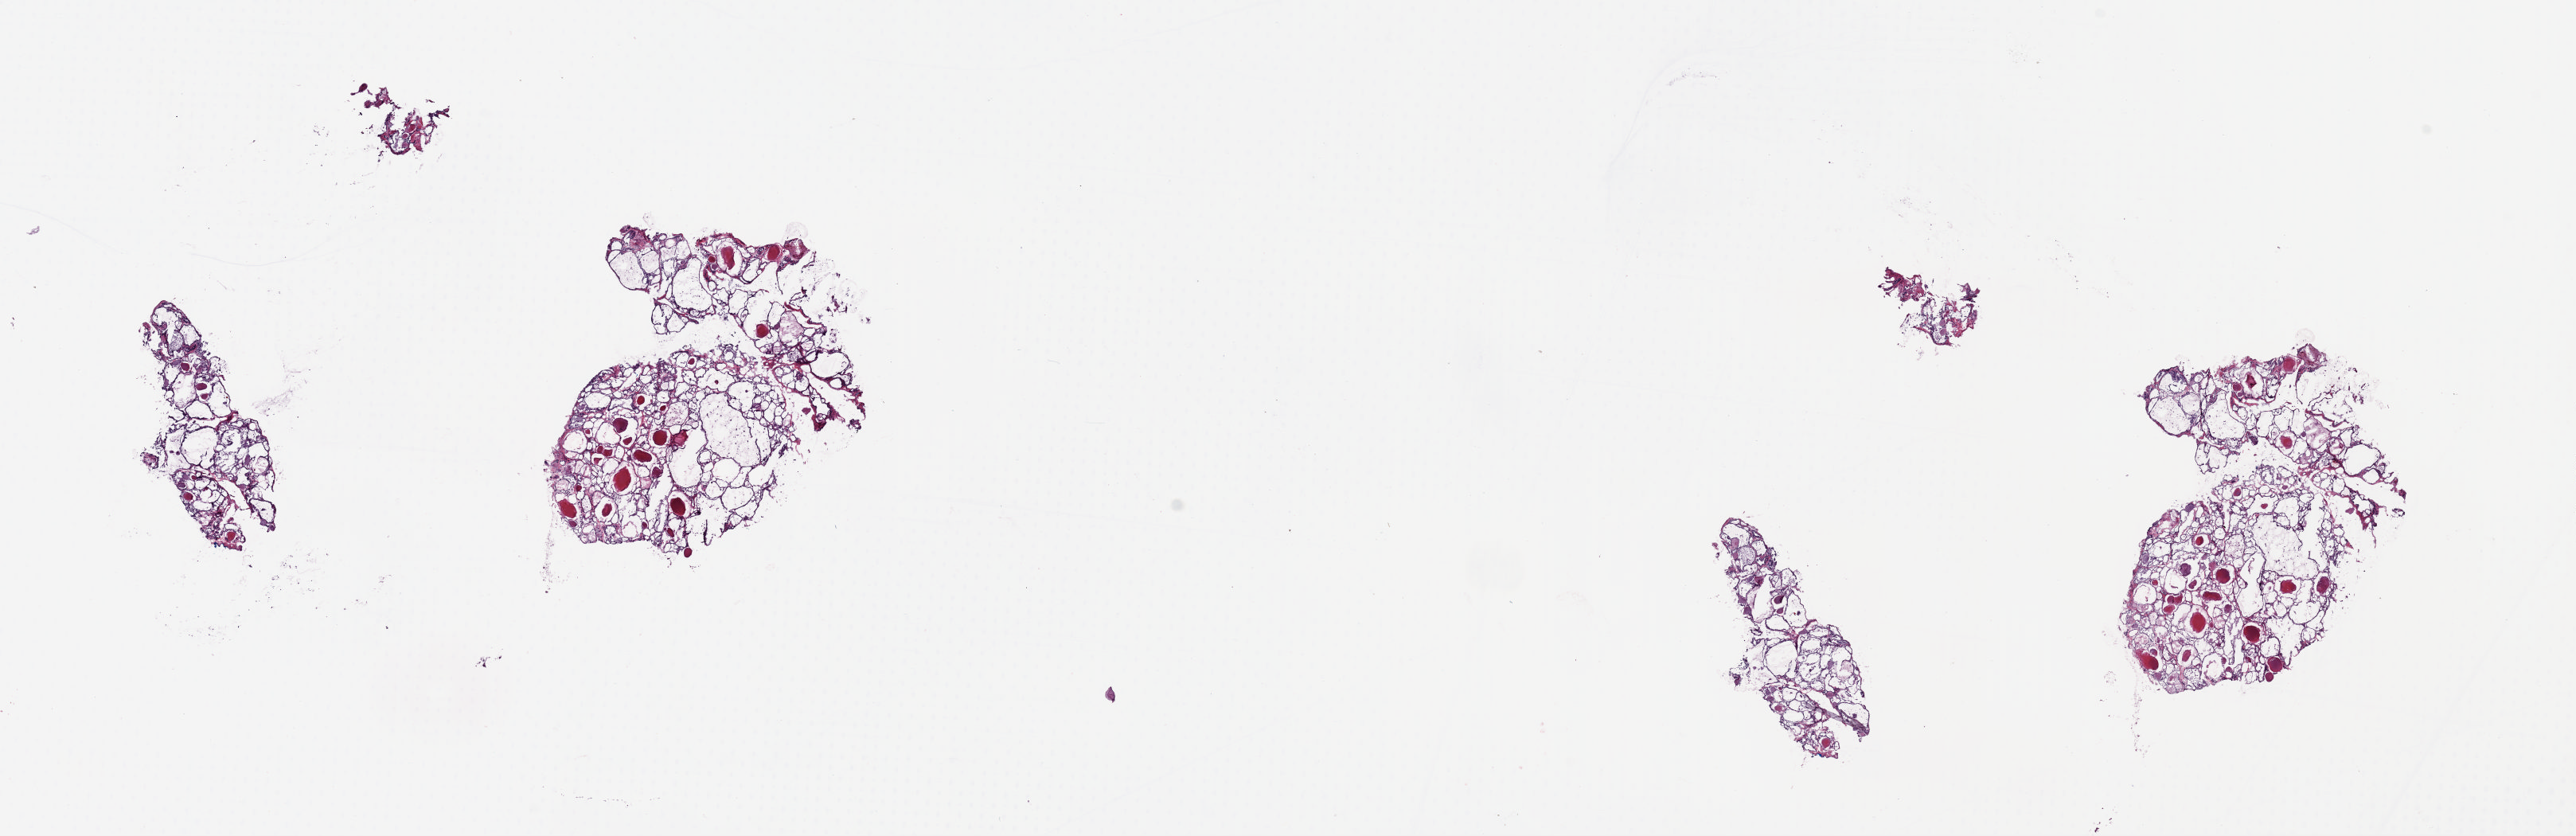
H&E-stained whole-slide image — a low-resolution overview of the entire scanned area, about 25.5 x 8.3 mm; frozen section; solid tissue normal (non-tumour tissue) sample from the thyroid. Patient: female, age at initial diagnosis 49 years. Slide review estimates, as recorded: tumour cells 0%, tumour nuclei 0%, normal cells 100%, stromal cells 0%, necrosis 0%. Inflammatory infiltration, as recorded: lymphocyte infiltration 1%, monocyte infiltration 1%, neutrophil infiltration 0%.
This section: solid tissue normal sample (biorepository sample class). Patient diagnosis: Papillary adenocarcinoma, NOS (thyroid gland).